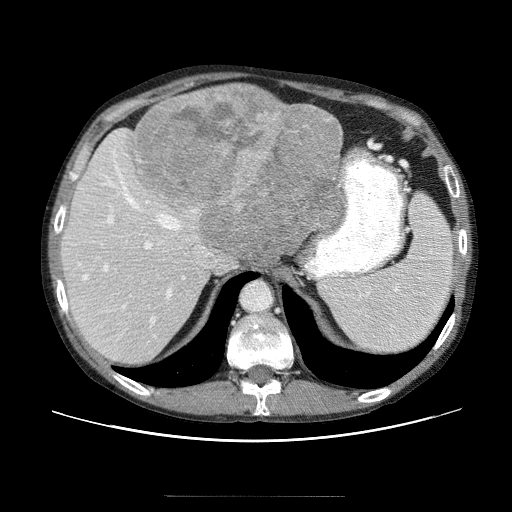
Contrast-enhanced abdominal CT (liver protocol), one axial slice. Slice 41 of 69 in the series (ordered by position). Soft-tissue window (W 400 / L 40 HU). 512 × 512 image matrix, field of view 380 × 380 mm. From the clinical record (not read from this slice): diagnosis: hepatocellular carcinoma (patient treated with transarterial chemoembolisation; whether this scan precedes or follows treatment is not stated here); TNM stage (as recorded): Stage-IVB; Child-Pugh class: B.
Structures marked on this image (semi-automatically segmented with operator editing):
- liver parenchyma outside the tumour (the mass and vessels are separate outlines, so this box may not span the whole liver): box from (x=58, y=100) to (x=342, y=368) px
- mass: (x=129, y=83)–(x=344, y=273)
- liver vessels: (x=97, y=152)–(x=213, y=343)